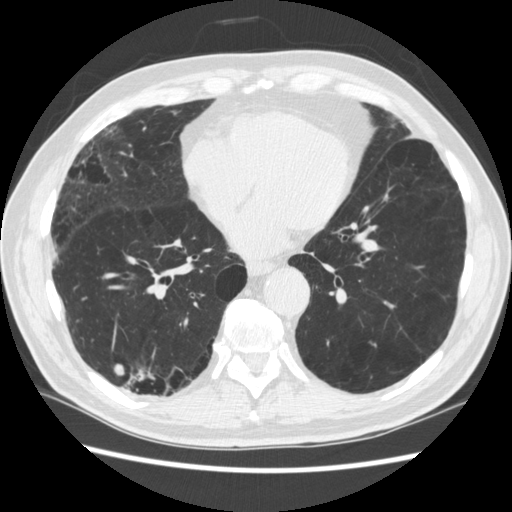
Low-dose screening chest CT, axial slice, third screening round (two years after baseline), lung window (W 1500 / L -600 HU), standard (soft-tissue) reconstruction kernel (STANDARD), 512 × 512 image matrix. Male, age 70 years at enrolment. Former smoker at enrolment.
Lesion marked by an expert reader, box from (x=129, y=359) to (x=177, y=413) px. The screening reader recorded 4 non-calcified nodules or masses ≥4 mm on this exam (right lower lobe, right lower lobe, left lower lobe, left lower lobe); which of them this box marks is not recorded. Official screen result: positive, other. Lung cancer was diagnosed 253 days after this screen: squamous cell carcinoma, NOS, right upper lobe, poorly differentiated (G3), stage IV (AJCC 6th edition).